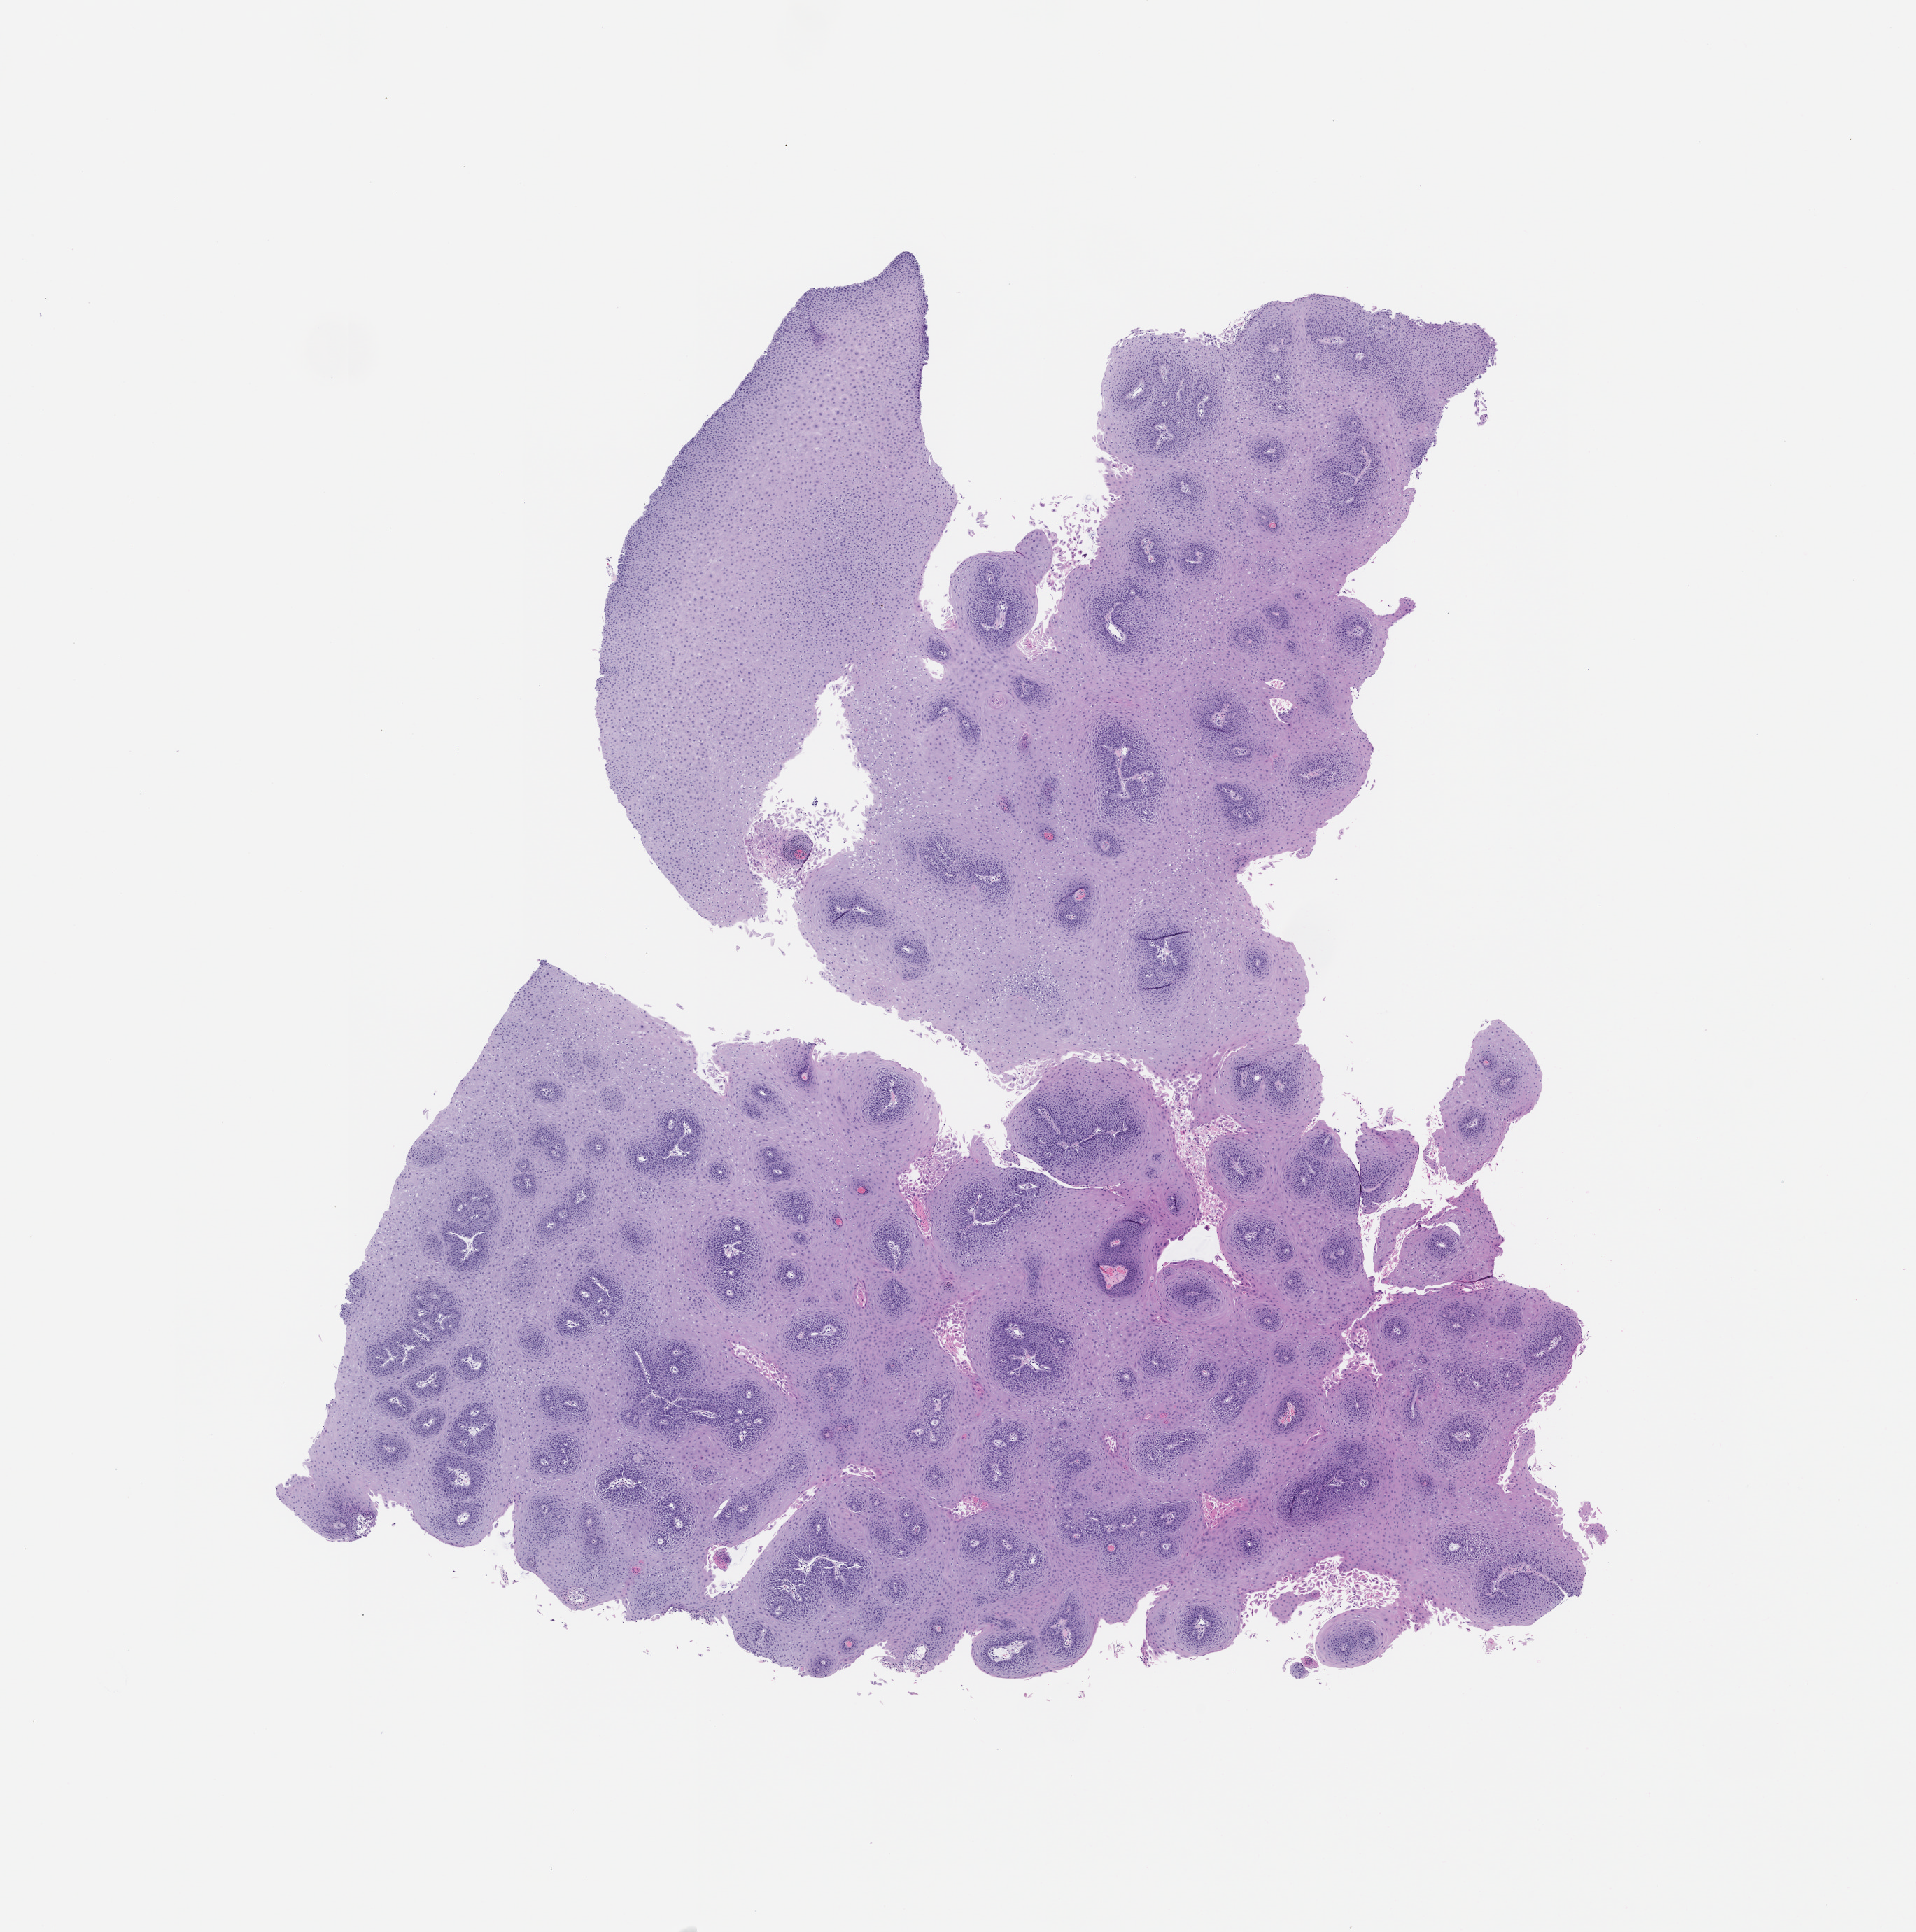
Whole-slide image, H&E: patient-derived xenograft (human tumor grown in a mouse), passage 1, whole scanned area (about 11.0 x 11.1 mm) shown as a low-resolution overview; FFPE section; originating tumor site category: bladder.
Originating patient diagnosis: Transitional Cell Carcinoma.